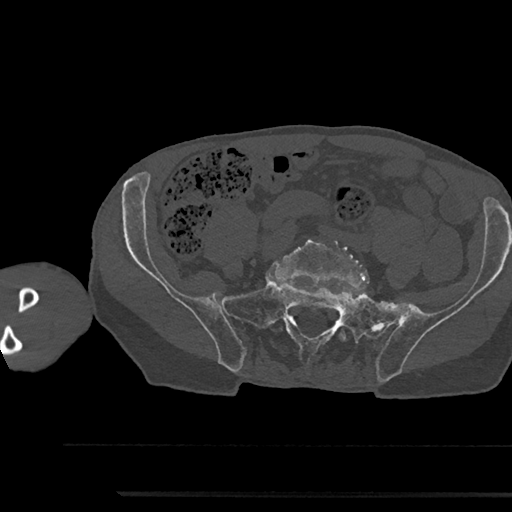
CT including the spine, one axial slice. Slice 310 of 797 in the series (ordered by position). 120 kVp. Bone window (W 1800 / L 400 HU). 0.5 mm slice thickness. 512 × 512 image matrix. Patient: male, 79 years. From the clinical record (not read from this slice): primary cancer: prostate.
Annotated regions visible in this slice (semi-automatic segmentation, software-assisted and operator-edited):
- L5 vertebra: bounding box <274,235,369,341> (left, top, right, bottom; pixels)